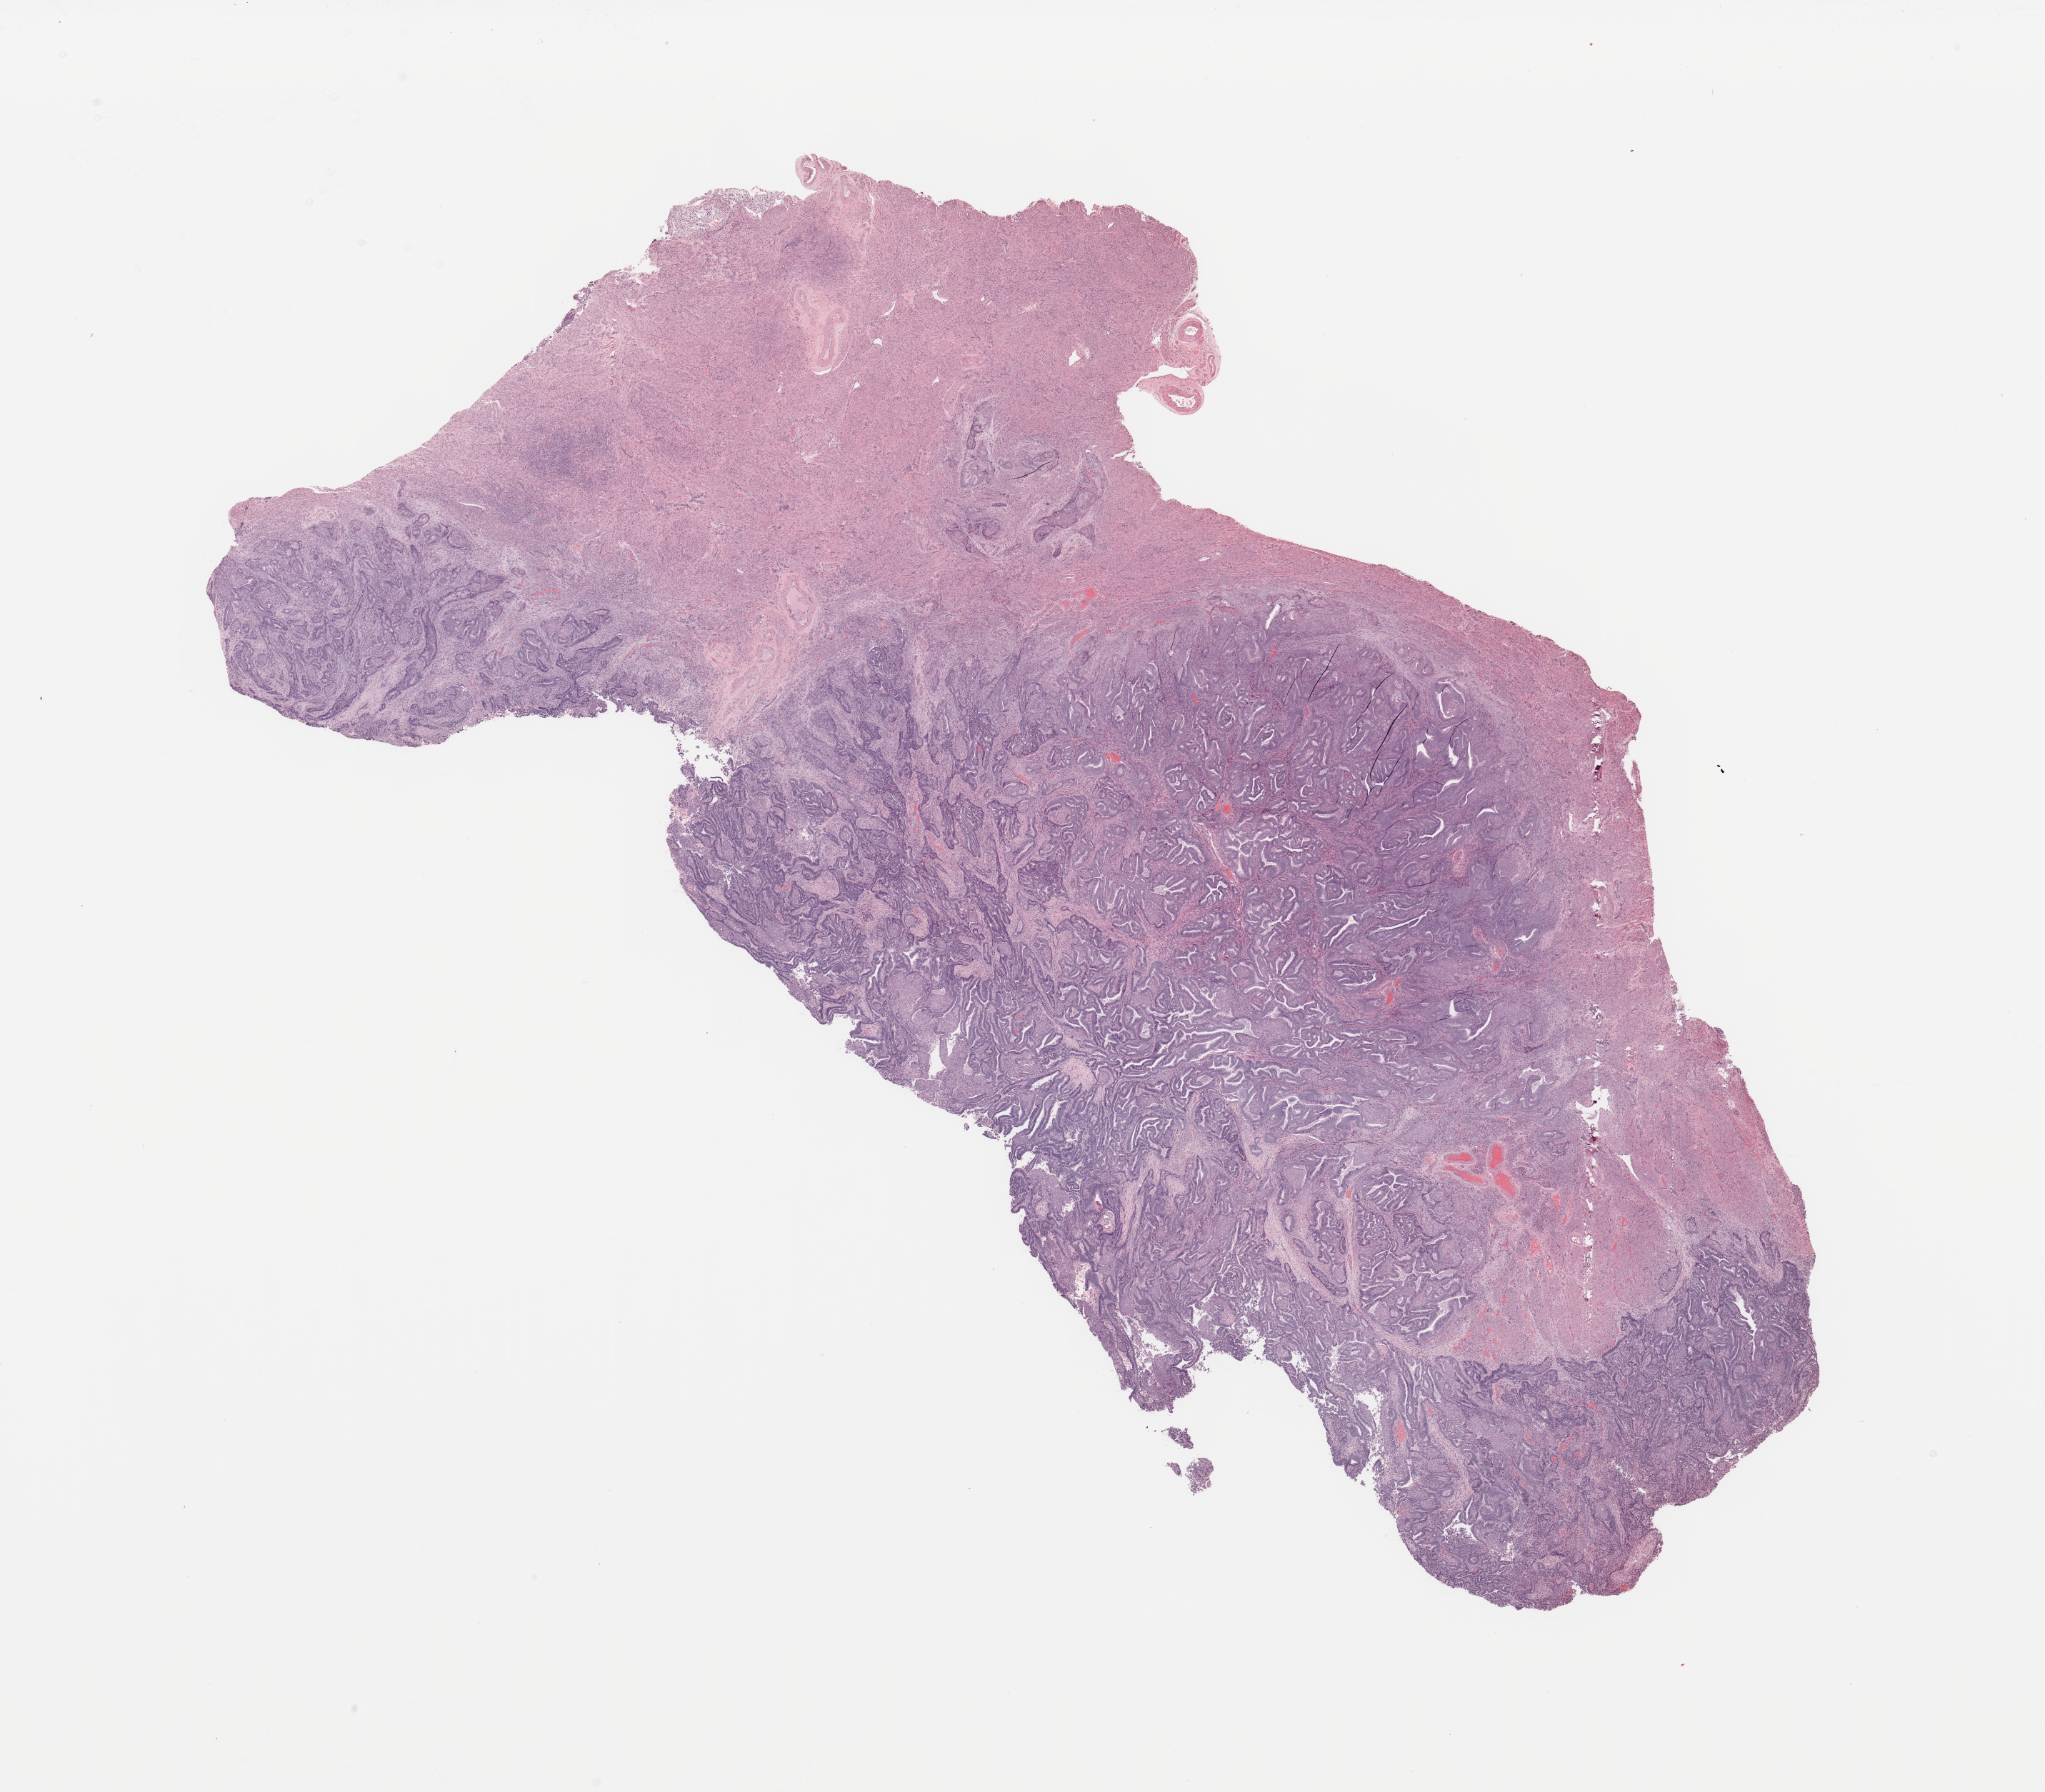
Whole-slide histology image, H&E-stained, shown as a low-resolution overview of the whole scanned area (about 22.6 x 19.8 mm). Tumour tissue sample, sampled site: uterus. Female, 54 y/o. Histologic grade: G1 (well differentiated). Pathologist review of this section (percent, as recorded): tumour nuclei 80%, necrosis 0%.
Histologic diagnosis: Endometrioid adenocarcinoma, NOS. AJCC pathologic stage: I.